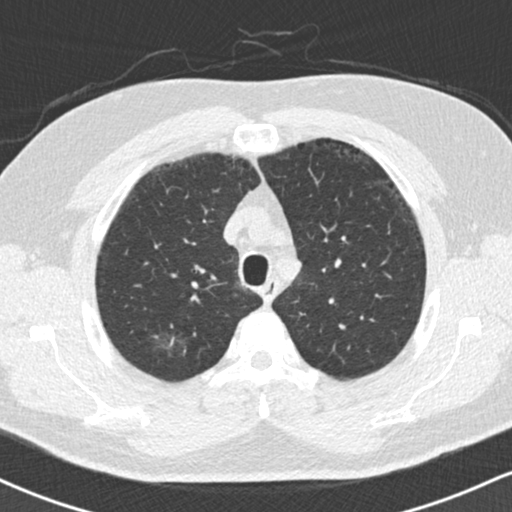
Low-dose screening chest CT, axial slice. Second screening round (one year after baseline). Lung window (W 1500 / L -600 HU). 2 mm slice thickness. 512 × 512 image matrix. Male, age 59 years at enrolment. Current smoker at enrolment.
Lesion marked by an expert reader, bounding box <152,313,203,365> (left, top, right, bottom; pixels). The exam's reader record, not a measurement of the box and not confirmed to be the same lesion: non-calcified nodule or mass ≥4 mm, right upper lobe, 18 × 16 mm, ground glass attenuation, pre-existing on the prior screen: yes. Official screen result: positive, no significant change: stable abnormalities potentially related to lung cancer, unchanged since the prior screening exam.